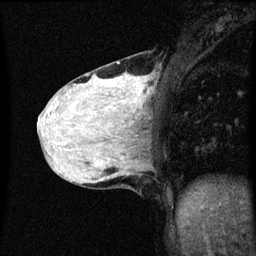
Breast MRI (dynamic contrast-enhanced), one sagittal slice; position 21 of 60 along the scan axis; dynamic contrast-enhanced series, image 2 of 3 at this slice position (ordered by acquisition); 1.5 T; TE 4.2 ms, TR 8.4 ms; 2 mm slice thickness; 256 × 256 image matrix, field of view 200 × 200 mm. Patient: female, 36 years.
Outlined on this slice (semi-automatically segmented with operator editing):
- analysis volume of interest (the breast-tissue region the enhancement analysis was run in; not a lesion): bounding box (x1, y1, x2, y2) in pixels: (48, 62, 151, 151)
- tumour enhancement mask (voxels above the 70 % enhancement threshold inside the analysis volume of interest): (128, 78, 145, 103)